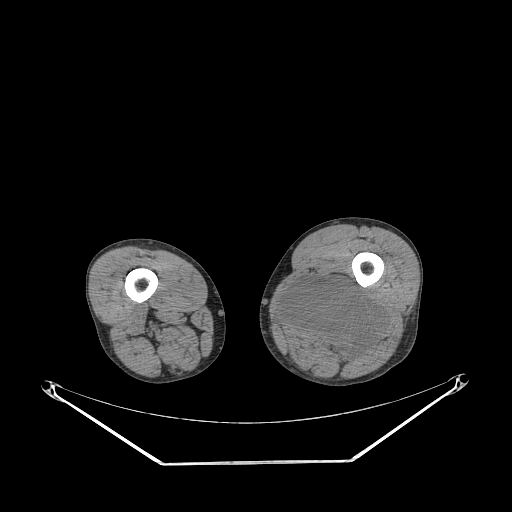
CT of an extremity soft-tissue mass (from a PET/CT study), one axial slice. Slice 221 of 267 in the series (ordered by position). 140 kVp. Soft-tissue window (W 400 / L 40 HU). 3.75 mm slice thickness. 512 × 512 image matrix, field of view 500 × 500 mm. Male patient. From the clinical record (not read from this slice): histological type: undifferentiated pleomorphic liposarcoma; grade: high; site of the primary tumour: left thigh.
Annotated regions visible in this slice (expert contour drawn on MRI and transferred to this co-registered scan by the dataset authors):
- gross tumour volume including surrounding oedema: bounding box (x1, y1, x2, y2) in pixels: (281, 278, 385, 359)
- gross tumour volume (mass): (281, 278, 385, 359)